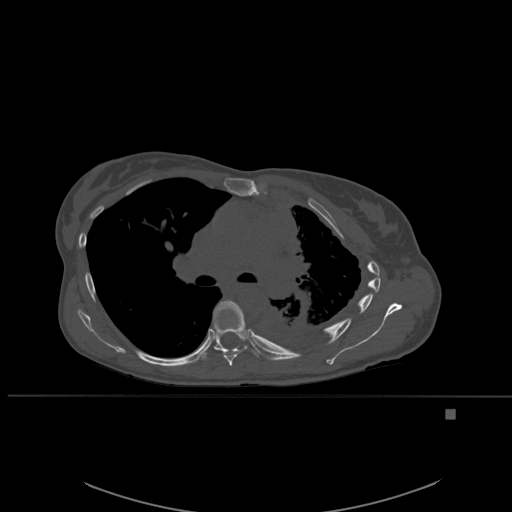
CT including the spine, one axial slice; position 375 of 537 along the scan axis; bone window (W 1800 / L 400 HU); 1.5 mm slice thickness; 512 × 512 image matrix, field of view 440 × 440 mm. Patient: female, 45 years. From the clinical record (not read from this slice): primary cancer: lung.
Structures marked on this image (semi-automatically segmented with operator editing):
- T6 vertebra: box from (x=213, y=300) to (x=246, y=366) px
- T7 vertebra: (x=199, y=304)–(x=267, y=360)